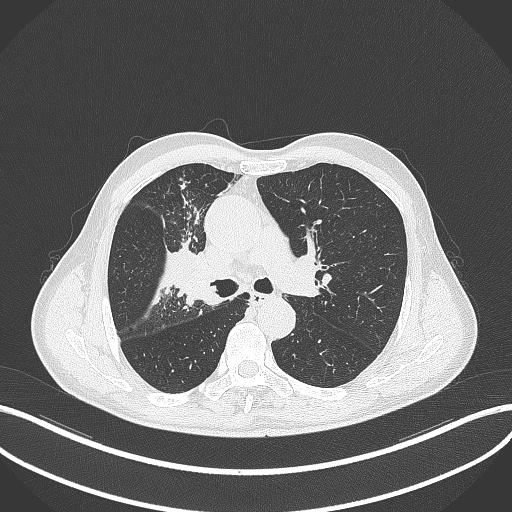
Chest CT, one axial slice. Position 309 of 490 along the scan axis. Reconstruction kernel B70f. Lung window (W 1500 / L -600 HU). 1 mm slice thickness. 512 × 512 image matrix, field of view 400 × 400 mm. Male patient, age 69 years. Case-level facts recorded for this patient, not image findings: clinical TNM (as recorded): T2a N0 M0.
Annotated regions visible in this slice (rectangle marked by the reading radiologist):
- lung tumour (recorded histology: adenocarcinoma): bounding box (x1, y1, x2, y2) in pixels: (167, 243, 222, 307)